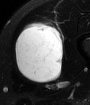
MRI of an extremity soft-tissue mass, one axial slice. Position 29 of 65 along the scan axis. T2-weighted fat-saturated. MR volume resampled by the dataset authors to the PET/CT grid (not the native acquisition matrix). 3.27 mm slice thickness. 90 × 105 image matrix. Male patient. Case-level facts recorded for this patient, not image findings: histological type: mixoid liposarcoma; grade: low; site of the primary tumour: left thigh.
Outlined on this slice (expert contour drawn on MRI and transferred to this co-registered scan by the dataset authors):
- gross tumour volume (mass): bounding box <14,21,62,81> (left, top, right, bottom; pixels)